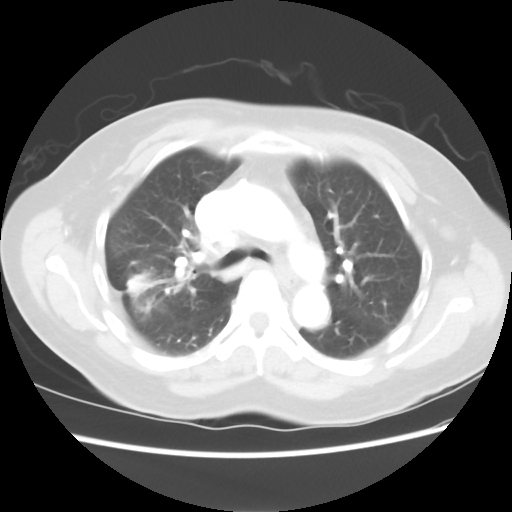
Chest CT, one axial slice; position 46 of 80 along the scan axis; 100 kVp; lung window (W 1500 / L -600 HU); 512 × 512 image matrix, field of view 342 × 342 mm. Female patient, age 67 years. Case-level facts recorded for this patient, not image findings: clinical TNM (as recorded): T1c N1 M0.
Outlined on this slice (bounding box drawn by a radiologist):
- lung tumour (recorded histology: adenocarcinoma): bounding box <123,263,162,318> (left, top, right, bottom; pixels)